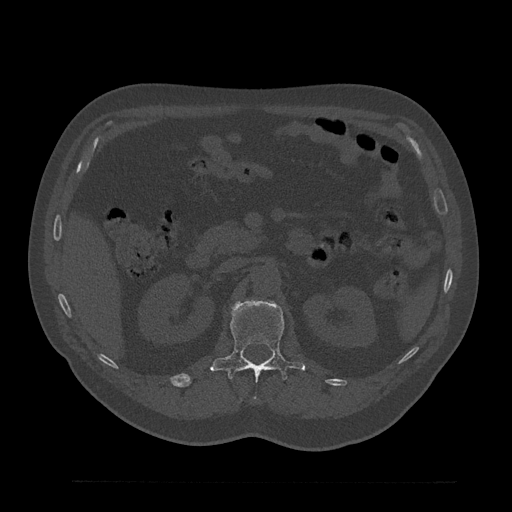
CT including the spine, one axial slice. Slice 167 of 797 in the series (ordered by position). Reconstruction kernel Br40s/3. Bone window (W 1800 / L 400 HU). 0.5 mm slice thickness. 512 × 512 image matrix. Male patient, age 61 years. Case-level facts recorded for this patient, not image findings: primary cancer: prostate.
Outlined on this slice (semi-automatic segmentation, software-assisted and operator-edited):
- L1 vertebra: bounding box [x1, y1, x2, y2] px = [211, 300, 305, 380]